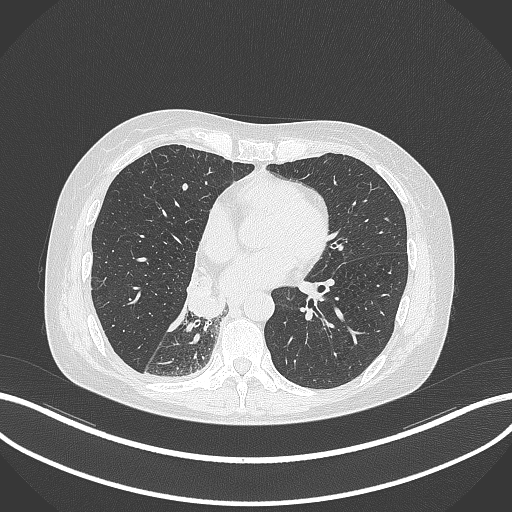
Chest CT, one axial slice; position 127 of 329 along the scan axis; reconstruction kernel B70f; lung window (W 1500 / L -600 HU); 1 mm slice thickness; 512 × 512 image matrix. Female patient, age 63 years. Case-level facts recorded for this patient, not image findings: clinical TNM (as recorded): T1c N0 M0.
Annotated regions visible in this slice (bounding box drawn by a radiologist):
- lung tumour (recorded histology: adenocarcinoma): box from (x=180, y=268) to (x=229, y=318) px